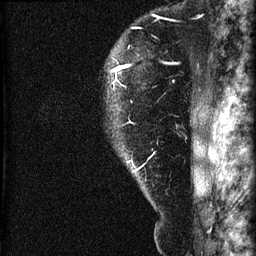
Breast MRI (dynamic contrast-enhanced), one sagittal slice. Slice 55 of 60 in the series (ordered by position). Dynamic contrast-enhanced series, image 2 of 3 at this slice position (ordered by acquisition). 1.5 T. TE 4.2 ms, TR 22.7 ms. 256 × 256 image matrix. Patient: female, 45 years. Case-level facts recorded for this patient, not image findings: setting: breast cancer imaged before/during neoadjuvant chemotherapy; receptor status: HR-positive, HER2-negative.
Annotated regions visible in this slice (semi-automatically segmented with operator editing):
- analysis volume of interest (the breast-tissue region the enhancement analysis was run in; not a lesion): bounding box <102,11,205,140> (left, top, right, bottom; pixels)
- tumour enhancement mask (voxels above the 90 % enhancement threshold inside the analysis volume of interest): <112,65,128,72>